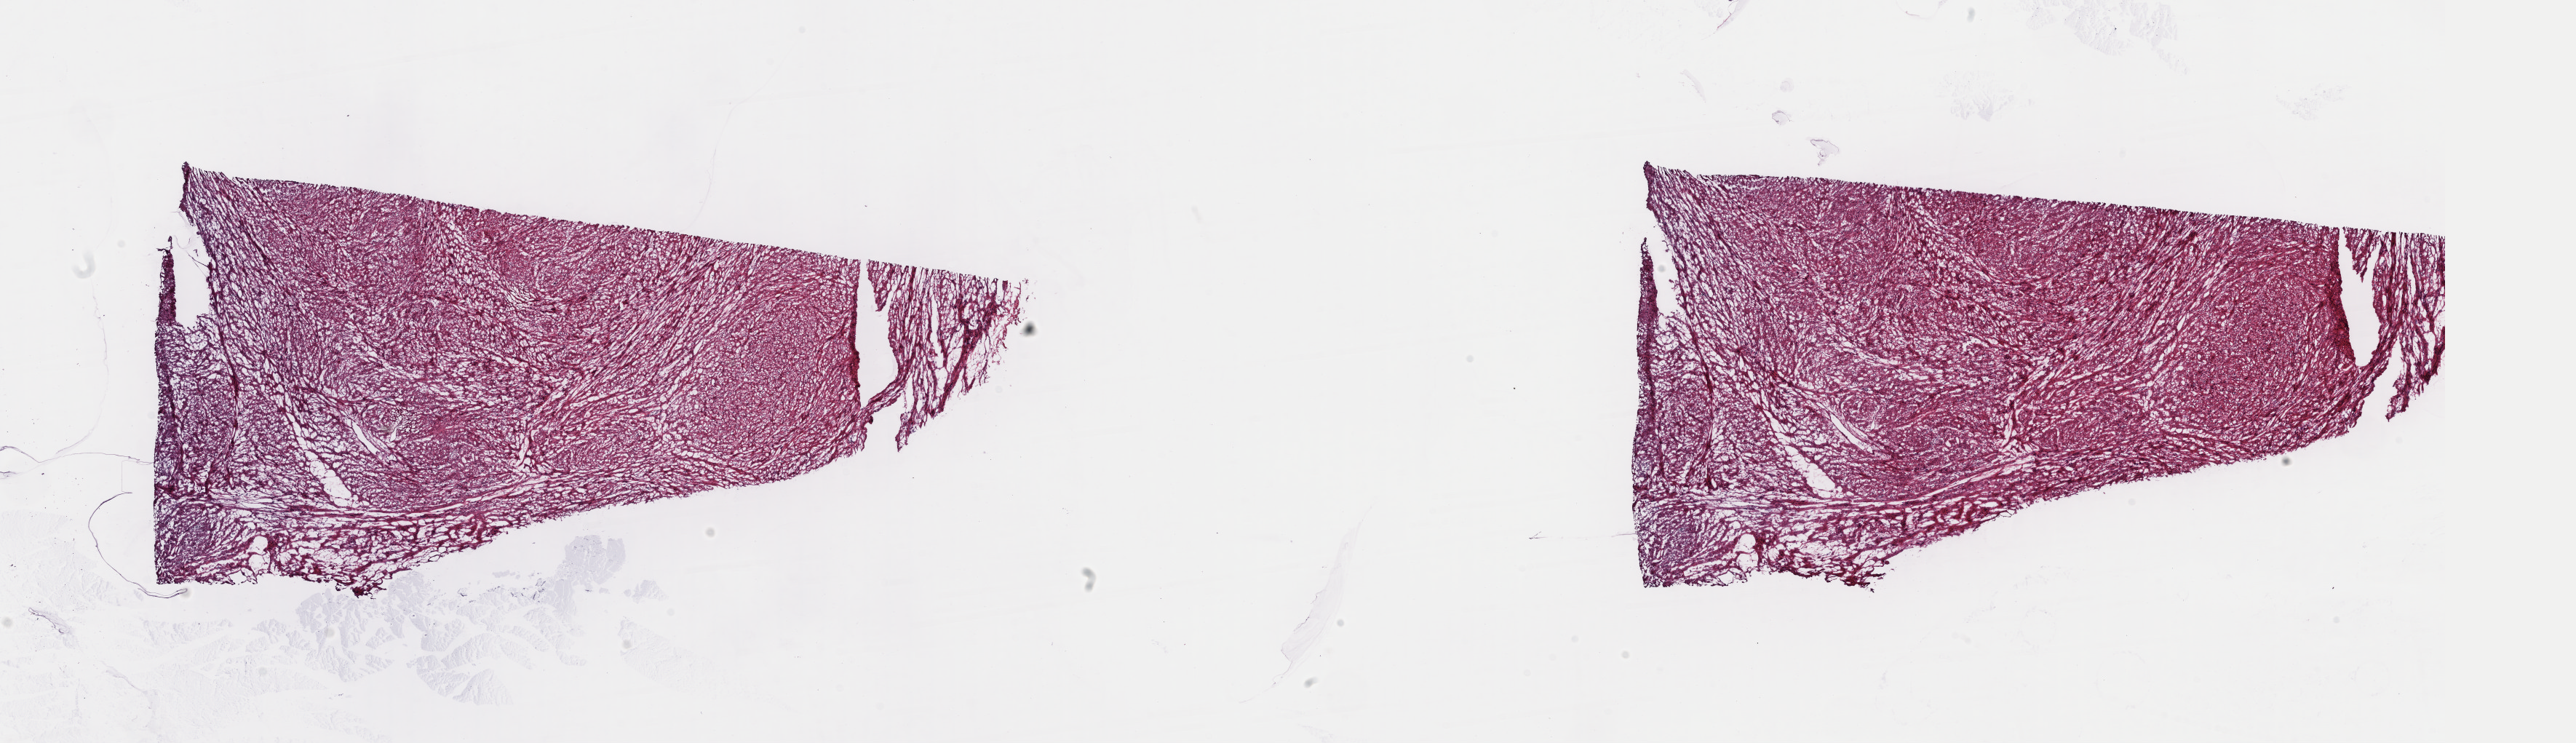
H&E-stained whole-slide image, low-resolution overview of the scanned area, about 27.9 x 8.1 mm (from a 40x scan). Frozen section. Retroperitoneum and peritoneum, primary tumour sample. Male patient; age at initial diagnosis 63 years. Slide review estimates, as recorded: tumour cells 85%, tumour nuclei 100%, normal cells 0%, stromal cells 15%, necrosis 0%. Infiltration values recorded for this section: lymphocyte infiltration 0%, monocyte infiltration 0%, neutrophil infiltration 0%.
* diagnosis: Leiomyosarcoma, NOS